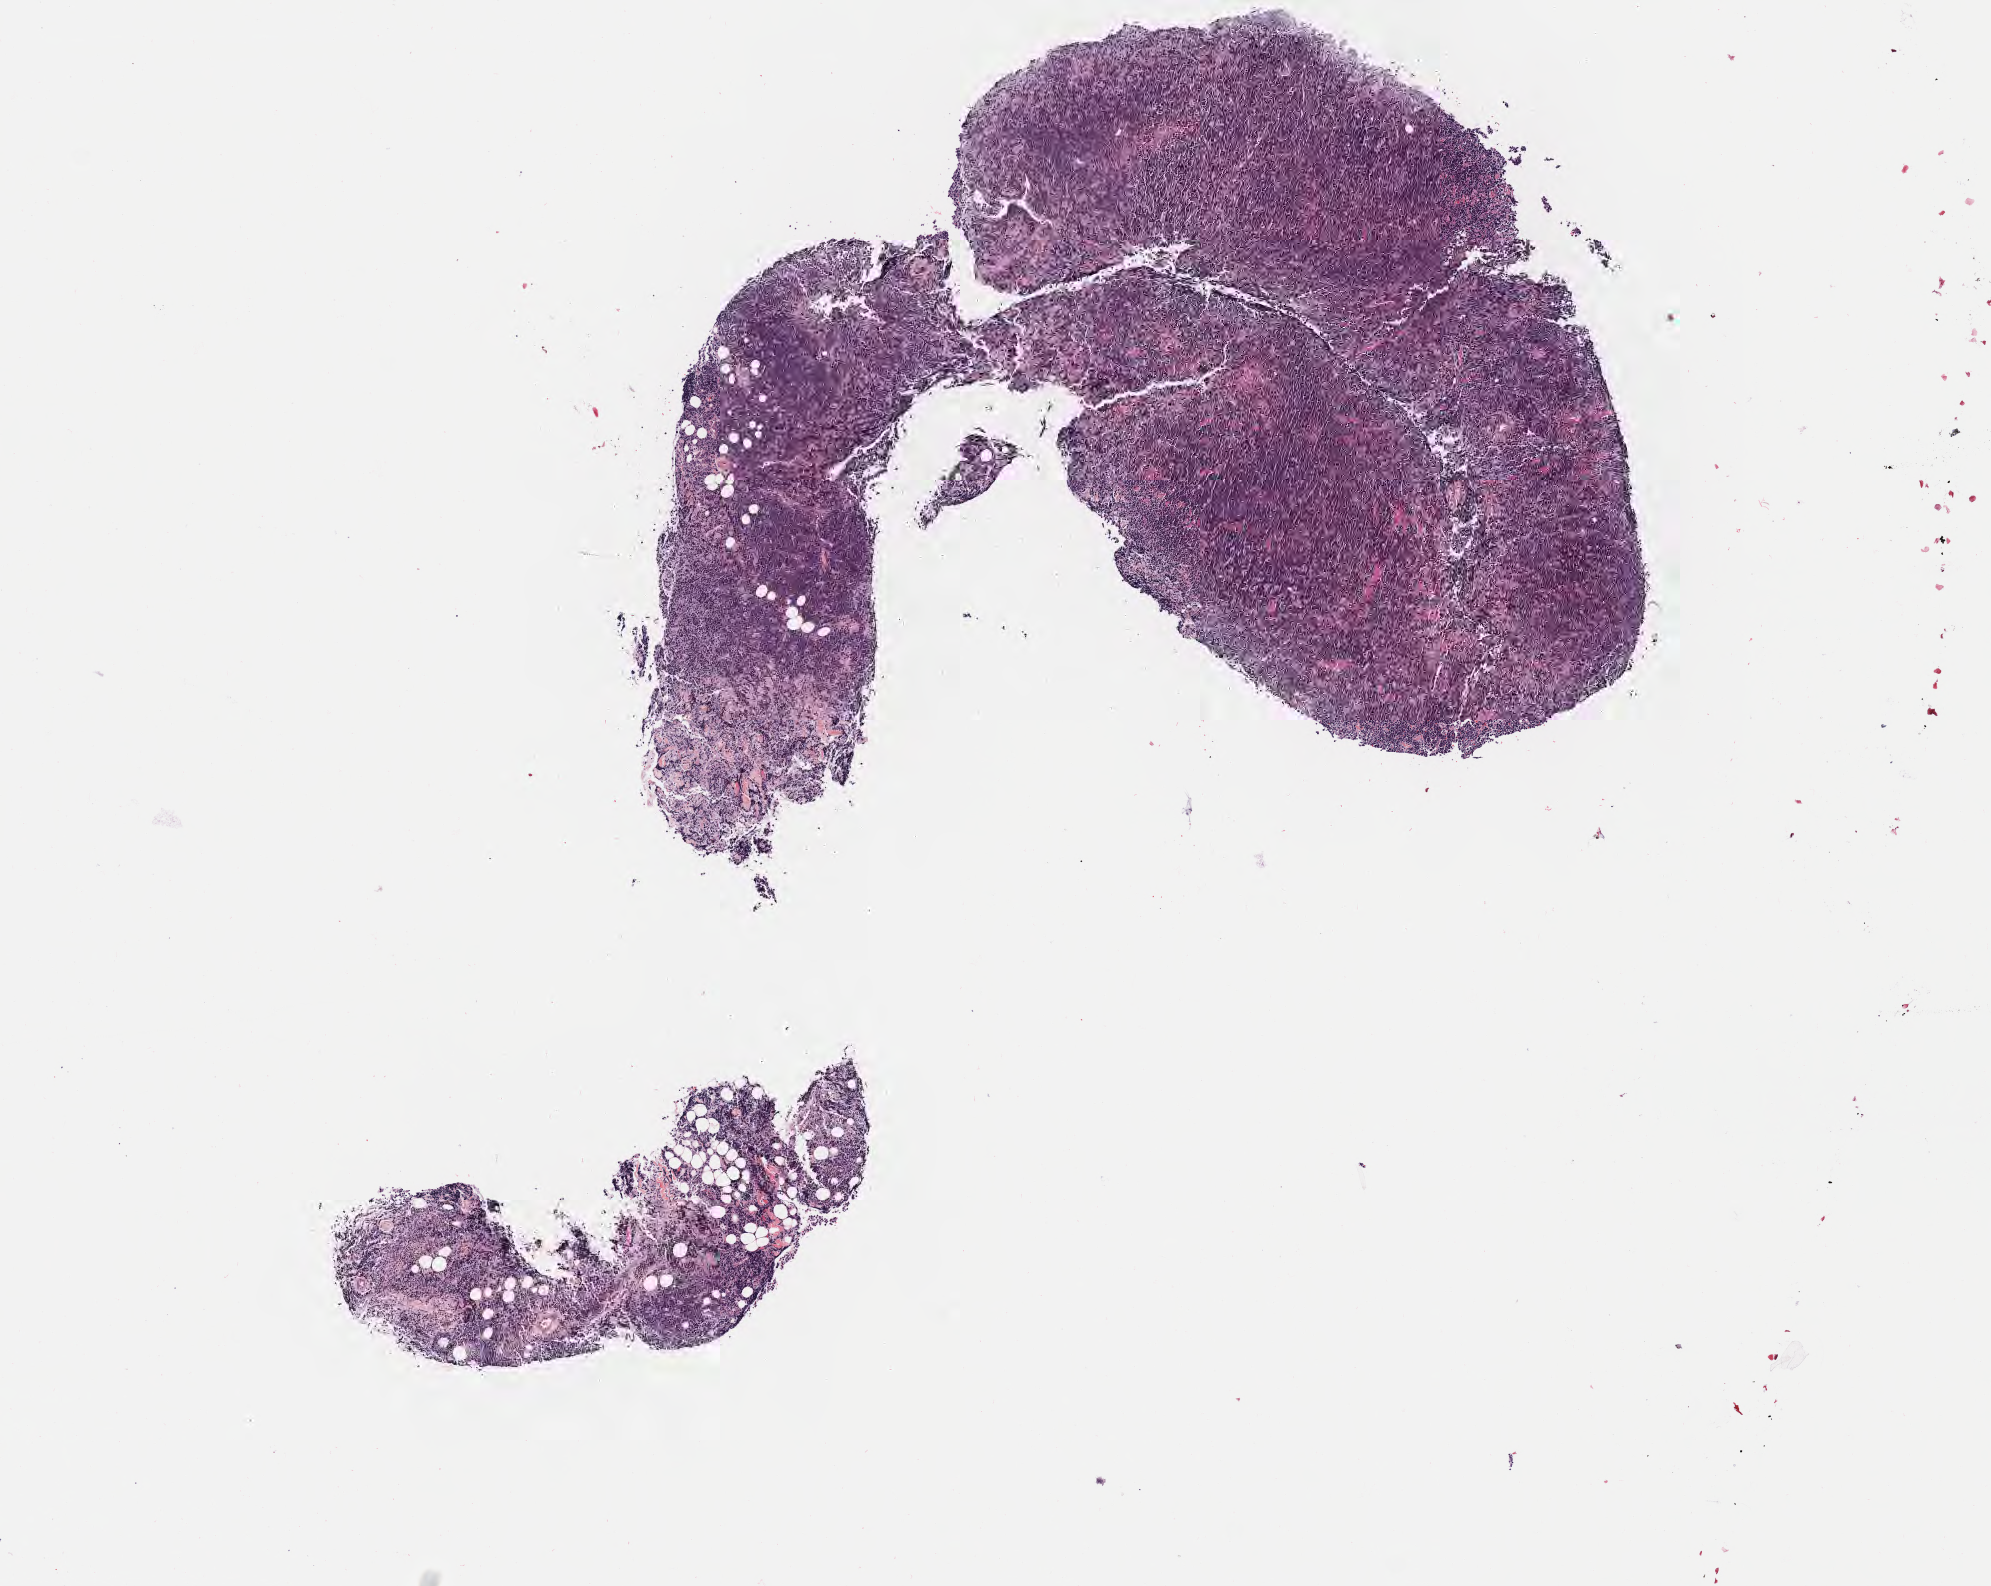
Haematoxylin and eosin whole-slide image, whole scanned area (about 8.1 x 6.4 mm) shown as a low-resolution overview. Tumor tissue. Anatomic site: head and neck. Female patient, aged 55.
Diagnosis: Burkitt lymphoma, NOS.